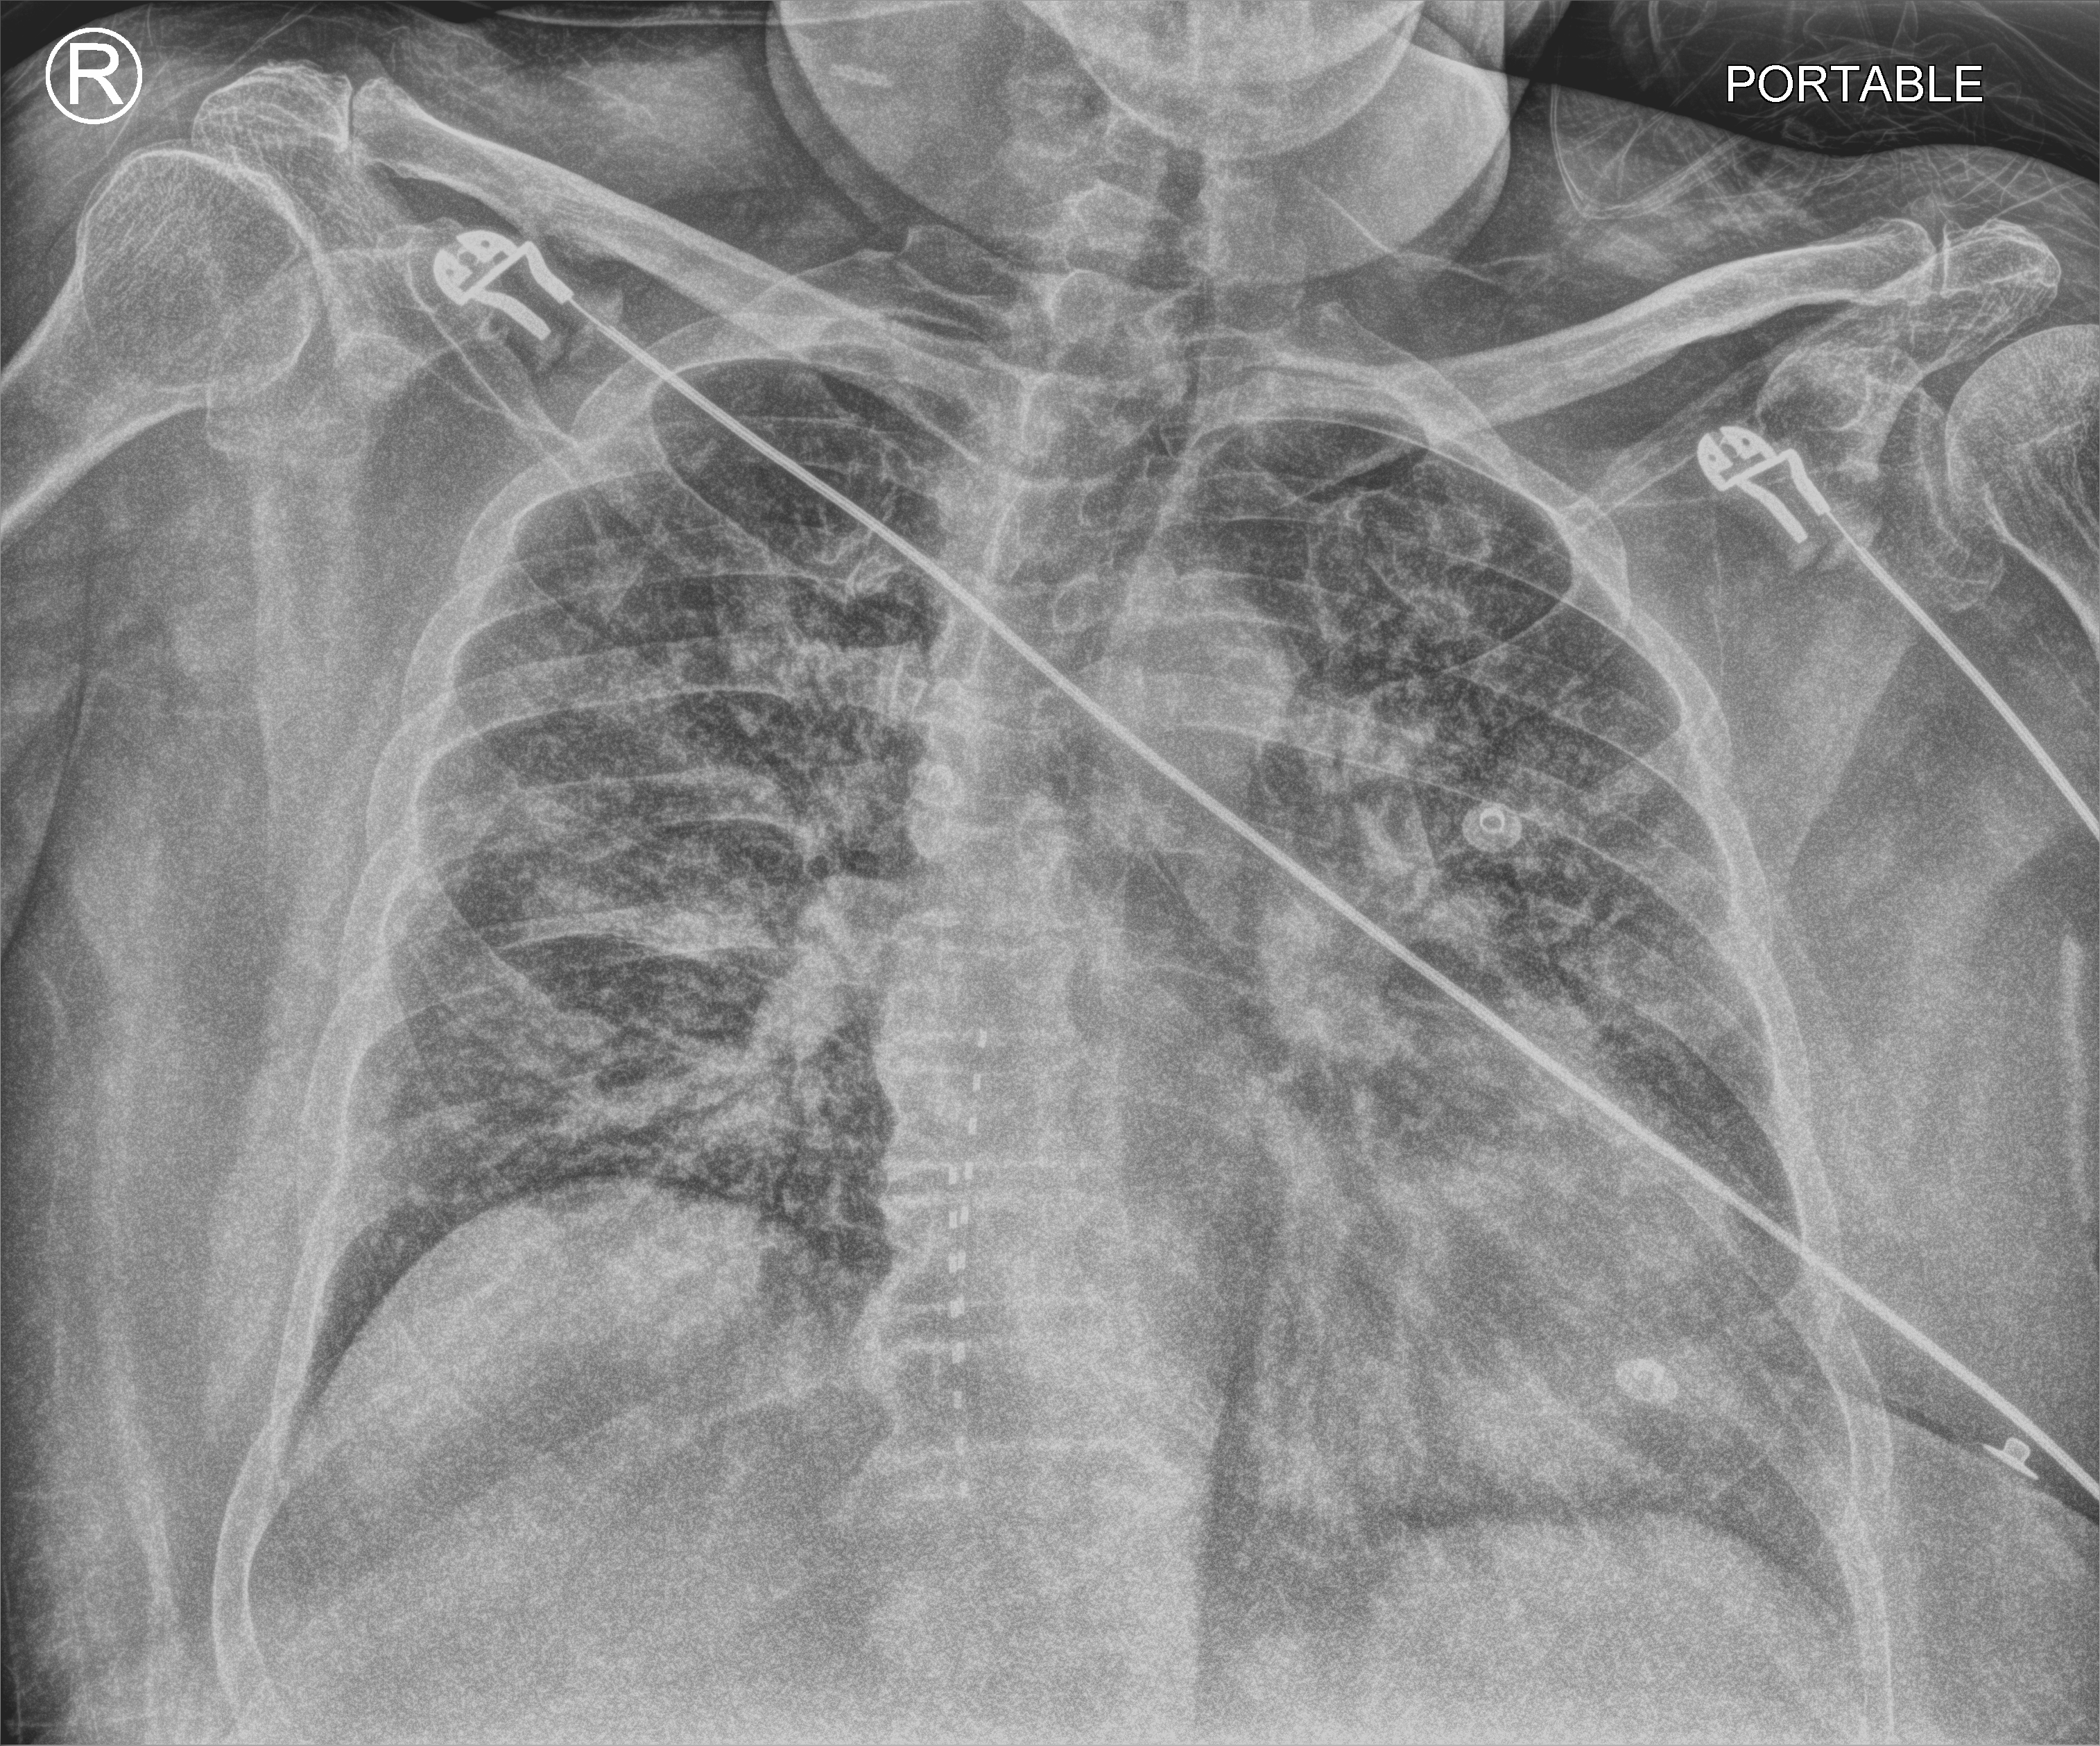
Portable chest radiograph, anteroposterior (AP) projection. Patient hospitalised with COVID-19; male, aged 60–74 years.
Hospital-stay facts (about this admission, not read from this image; timing relative to this image not recorded): mechanically ventilated during this hospital stay: no; admitted to intensive care during this hospital stay: no.